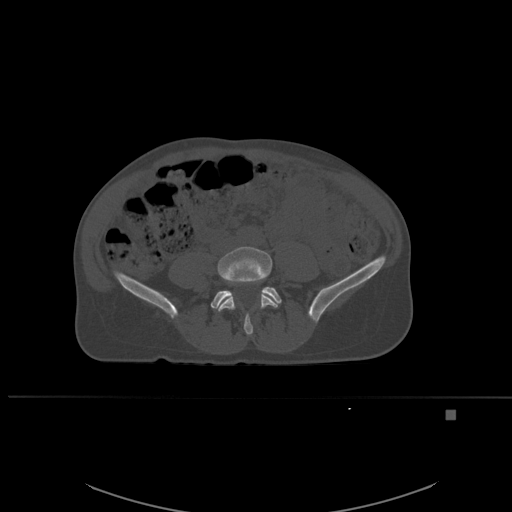
CT including the spine, one axial slice; bone window (W 1800 / L 400 HU); 1.5 mm slice thickness; 512 × 512 image matrix. Patient: female, 45 years. Case-level facts recorded for this patient, not image findings: primary cancer: lung.
Outlined on this slice (semi-automatically segmented with operator editing):
- L4 vertebra: bounding box [x1, y1, x2, y2] px = [214, 246, 278, 335]
- L5 vertebra: [210, 287, 282, 308]